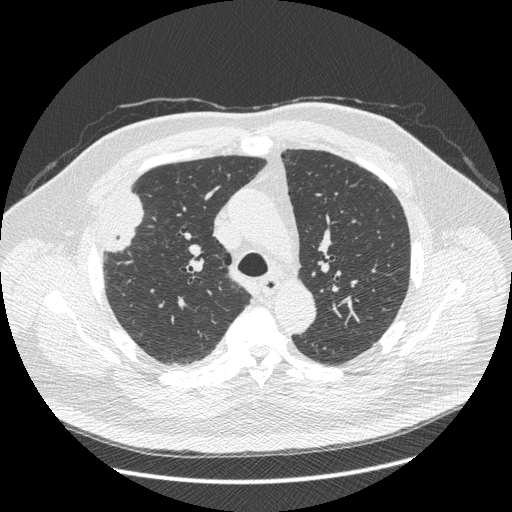
Low-dose screening chest CT, one axial slice; position 296 of 426 along the scan axis; reconstruction kernel STANDARD; 120 kVp; lung window (W 1500 / L -600 HU); 512 × 512 image matrix.
Structures marked on this image (expert manual segmentation):
- lesion 1 (tumor, upper lobe of right lung): bounding box <106,192,143,252> (left, top, right, bottom; pixels)